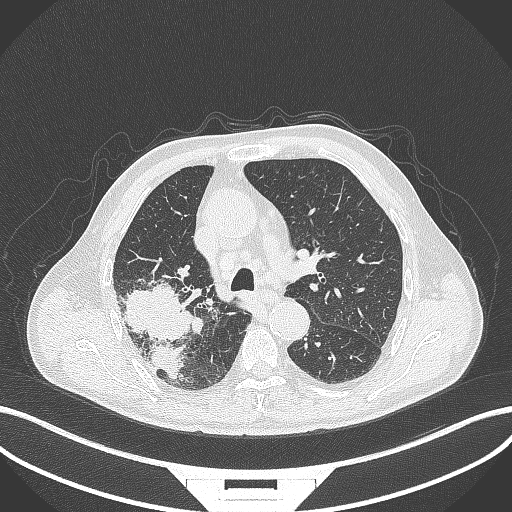
Chest CT, one axial slice. Position 277 of 429 along the scan axis. Reconstruction kernel B70f. Lung window (W 1500 / L -600 HU). 1 mm slice thickness. 512 × 512 image matrix, field of view 400 × 400 mm. Male patient, age 72 years. Case-level facts recorded for this patient, not image findings: clinical TNM (as recorded): T3 N2 M0.
Annotated regions visible in this slice (rectangle marked by the reading radiologist):
- lung tumour (recorded histology: adenocarcinoma): bounding box (x1, y1, x2, y2) in pixels: (118, 279, 205, 384)